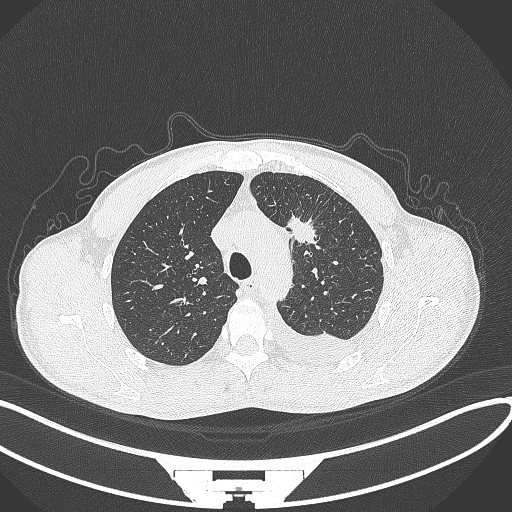
Chest CT, one axial slice. Lung window (W 1500 / L -600 HU). 512 × 512 image matrix, field of view 400 × 400 mm. Patient: male, 49 years. From the clinical record (not read from this slice): clinical TNM (as recorded): T1c N1 M1.
Outlined on this slice (bounding box drawn by a radiologist):
- lung tumour (recorded histology: adenocarcinoma): bounding box <282,214,320,253> (left, top, right, bottom; pixels)